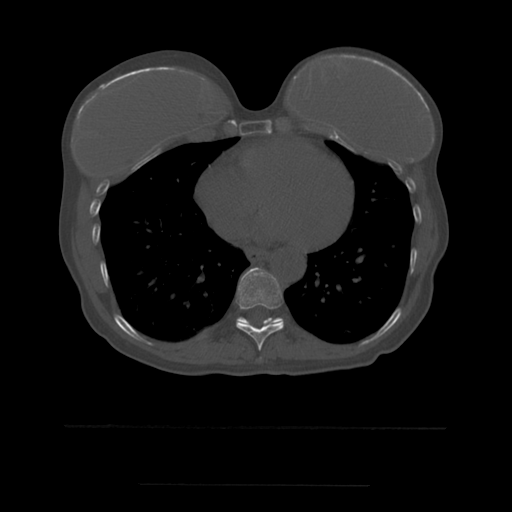
CT including the spine, one axial slice. Slice 316 of 544 in the series (ordered by position). Bone window (W 1800 / L 400 HU). 1.25 mm slice thickness. 512 × 512 image matrix, field of view 350 × 350 mm. Patient age 58 years. Case-level facts recorded for this patient, not image findings: primary cancer: lung.
Outlined on this slice (semi-automatic segmentation, software-assisted and operator-edited):
- T10 vertebra: bounding box <238,317,281,326> (left, top, right, bottom; pixels)
- T9 vertebra: <236,268,284,351>